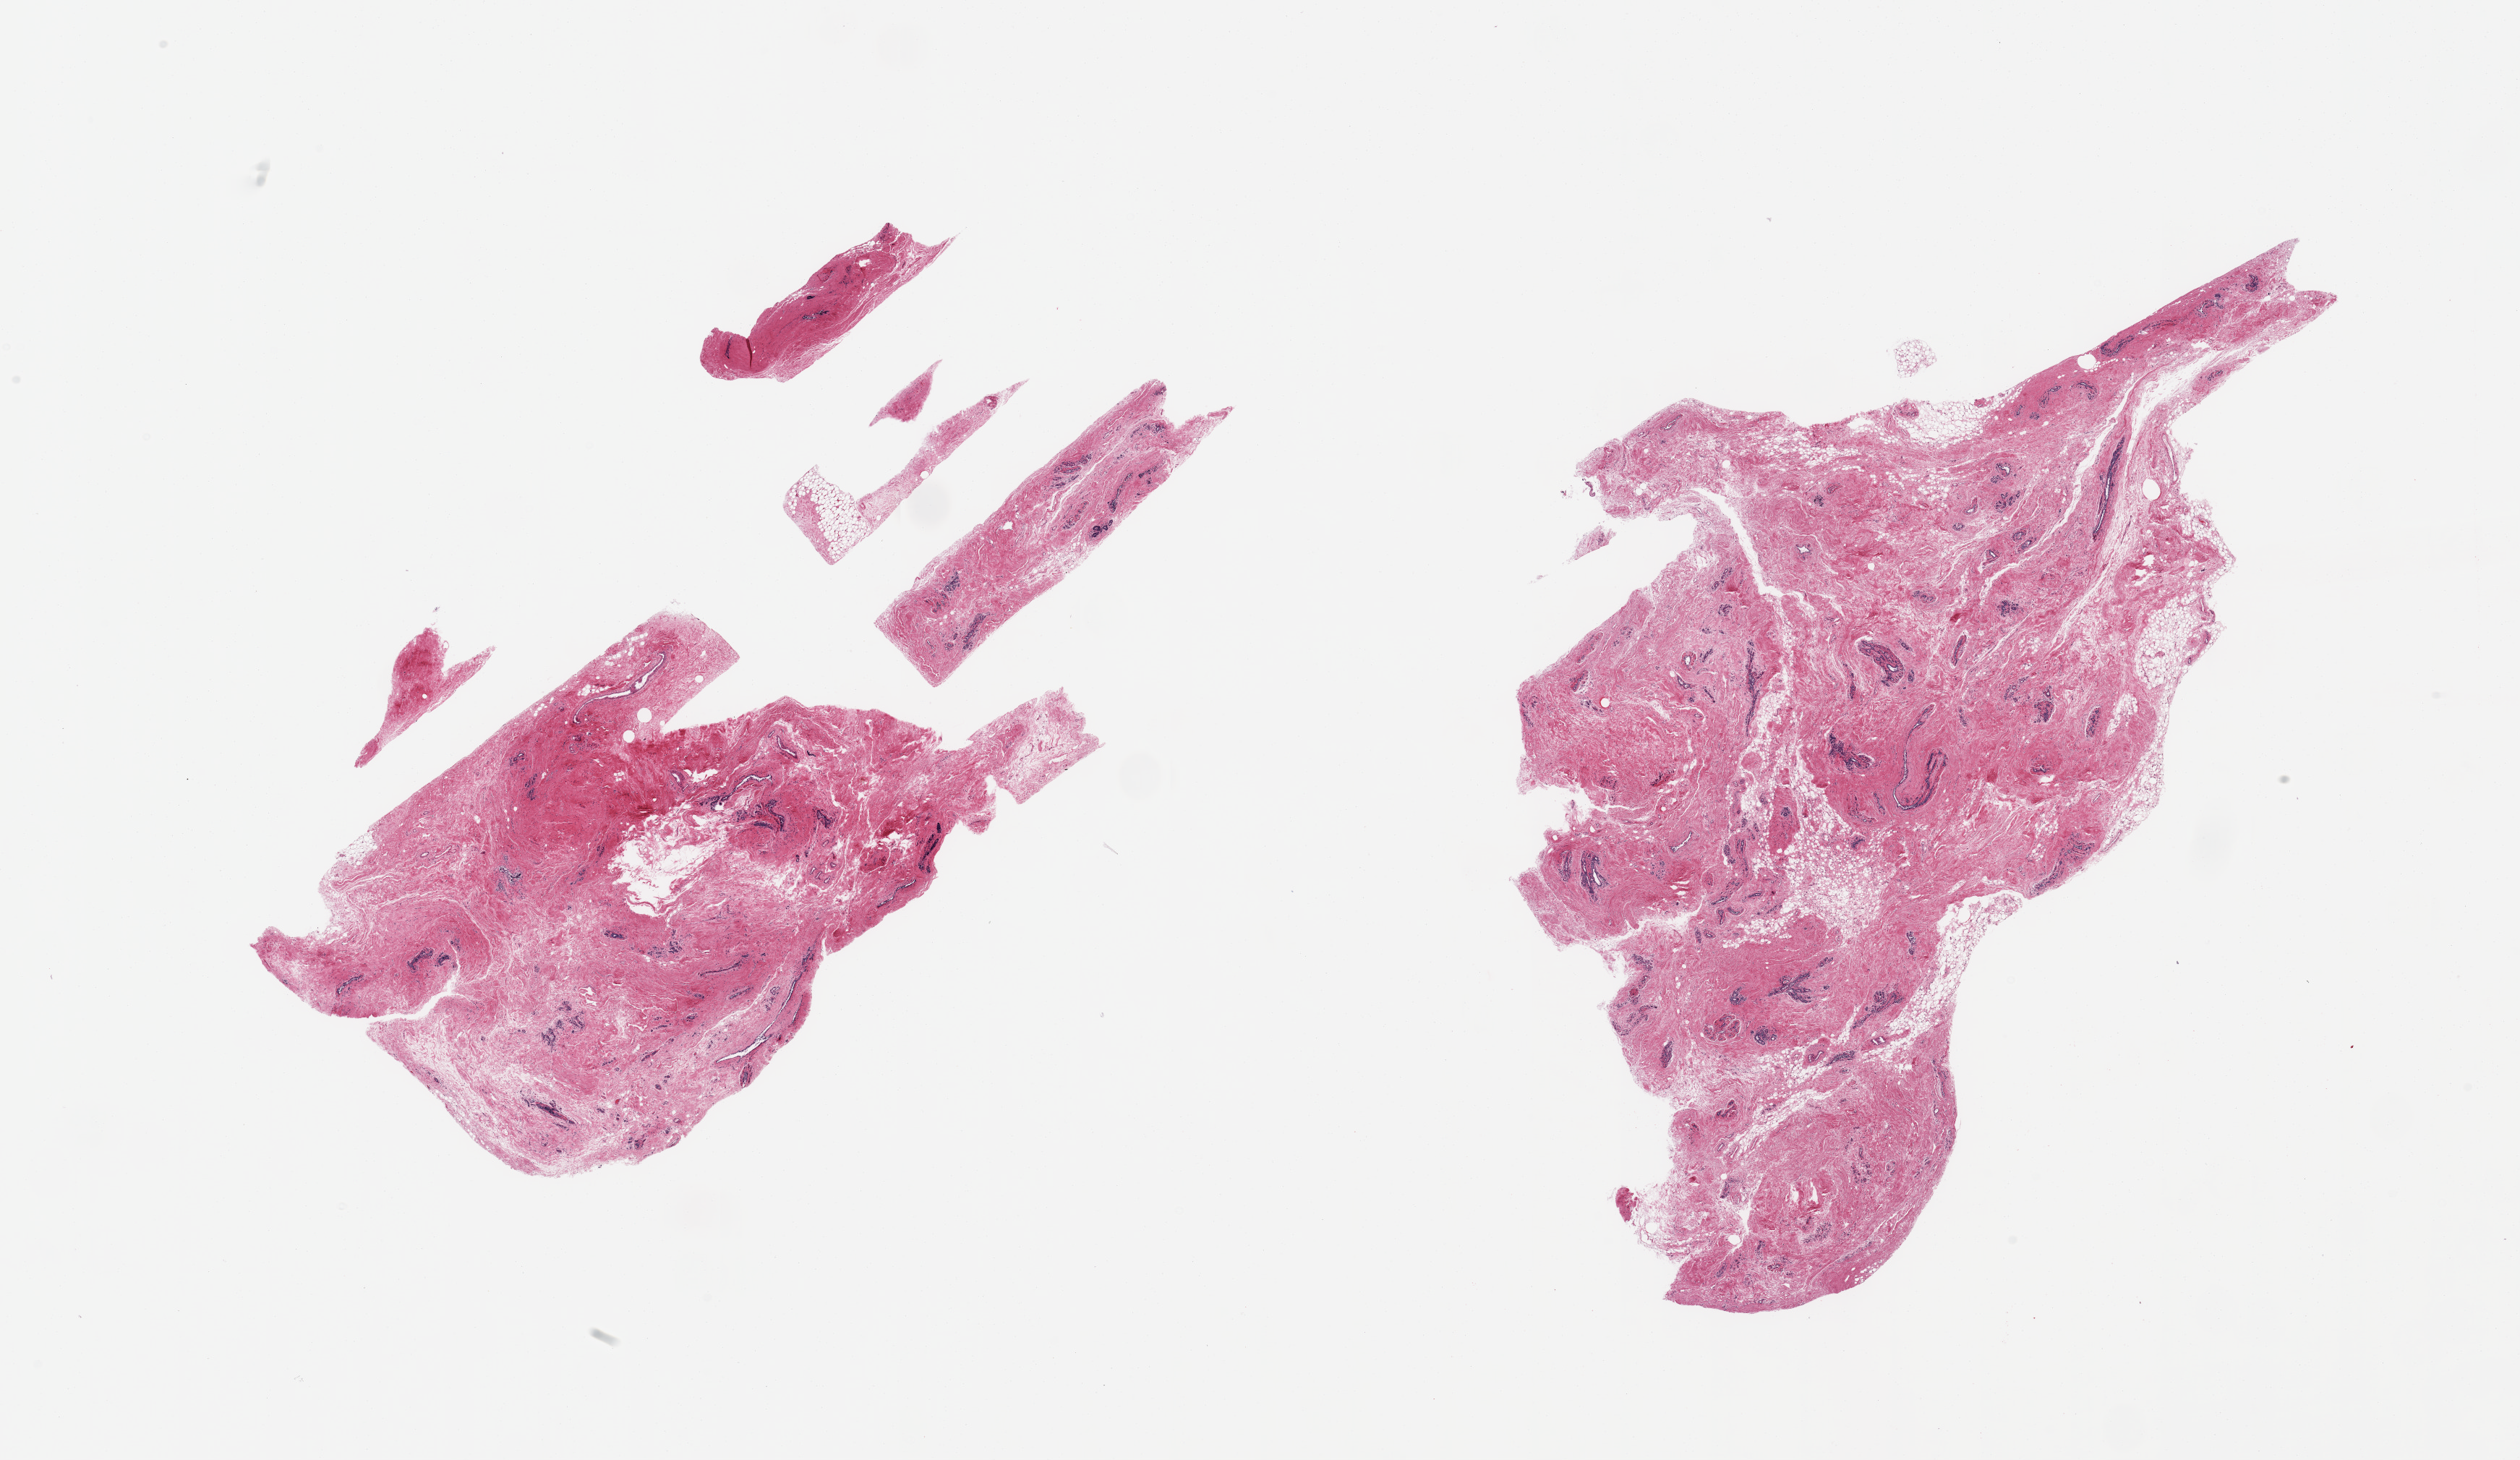
Haematoxylin and eosin whole-slide image, brightfield — a low-resolution overview of the entire scanned area, about 27.6 x 16.0 mm (from a 20x scan). PAXgene-fixed, paraffin-embedded tissue. Section of breast (target tissue). Tissue donor sample. Donor sex: female.
Review note (as recorded): 2 pieces, atrophic ductal/lobular elements.